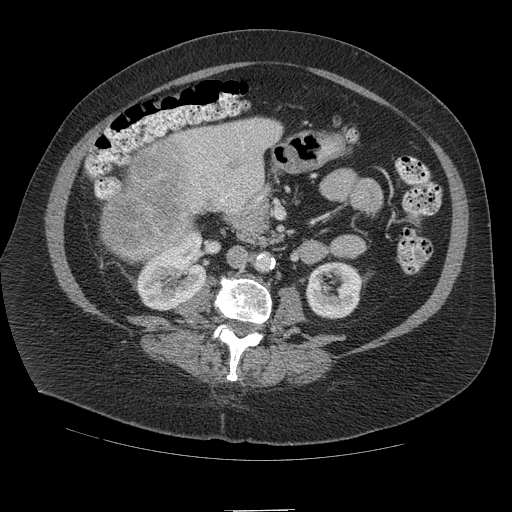
Contrast-enhanced abdominal CT (liver protocol), one axial slice. Position 33 of 109 along the scan axis. Reconstruction kernel STANDARD. 140 kVp. Soft-tissue window (W 400 / L 40 HU). 512 × 512 image matrix, field of view 420 × 420 mm. From the clinical record (not read from this slice): diagnosis: hepatocellular carcinoma (patient treated with transarterial chemoembolisation; whether this scan precedes or follows treatment is not stated here); TNM stage (as recorded): Stage-IVB; Child-Pugh class: A; tumour nodularity: multinodular.
Annotated regions visible in this slice (semi-automatic segmentation, software-assisted and operator-edited):
- liver parenchyma outside the tumour (the mass and vessels are separate outlines, so this box may not span the whole liver): bounding box <119,118,282,236> (left, top, right, bottom; pixels)
- mass: <98,137,199,261>
- liver vessels: <192,143,262,210>